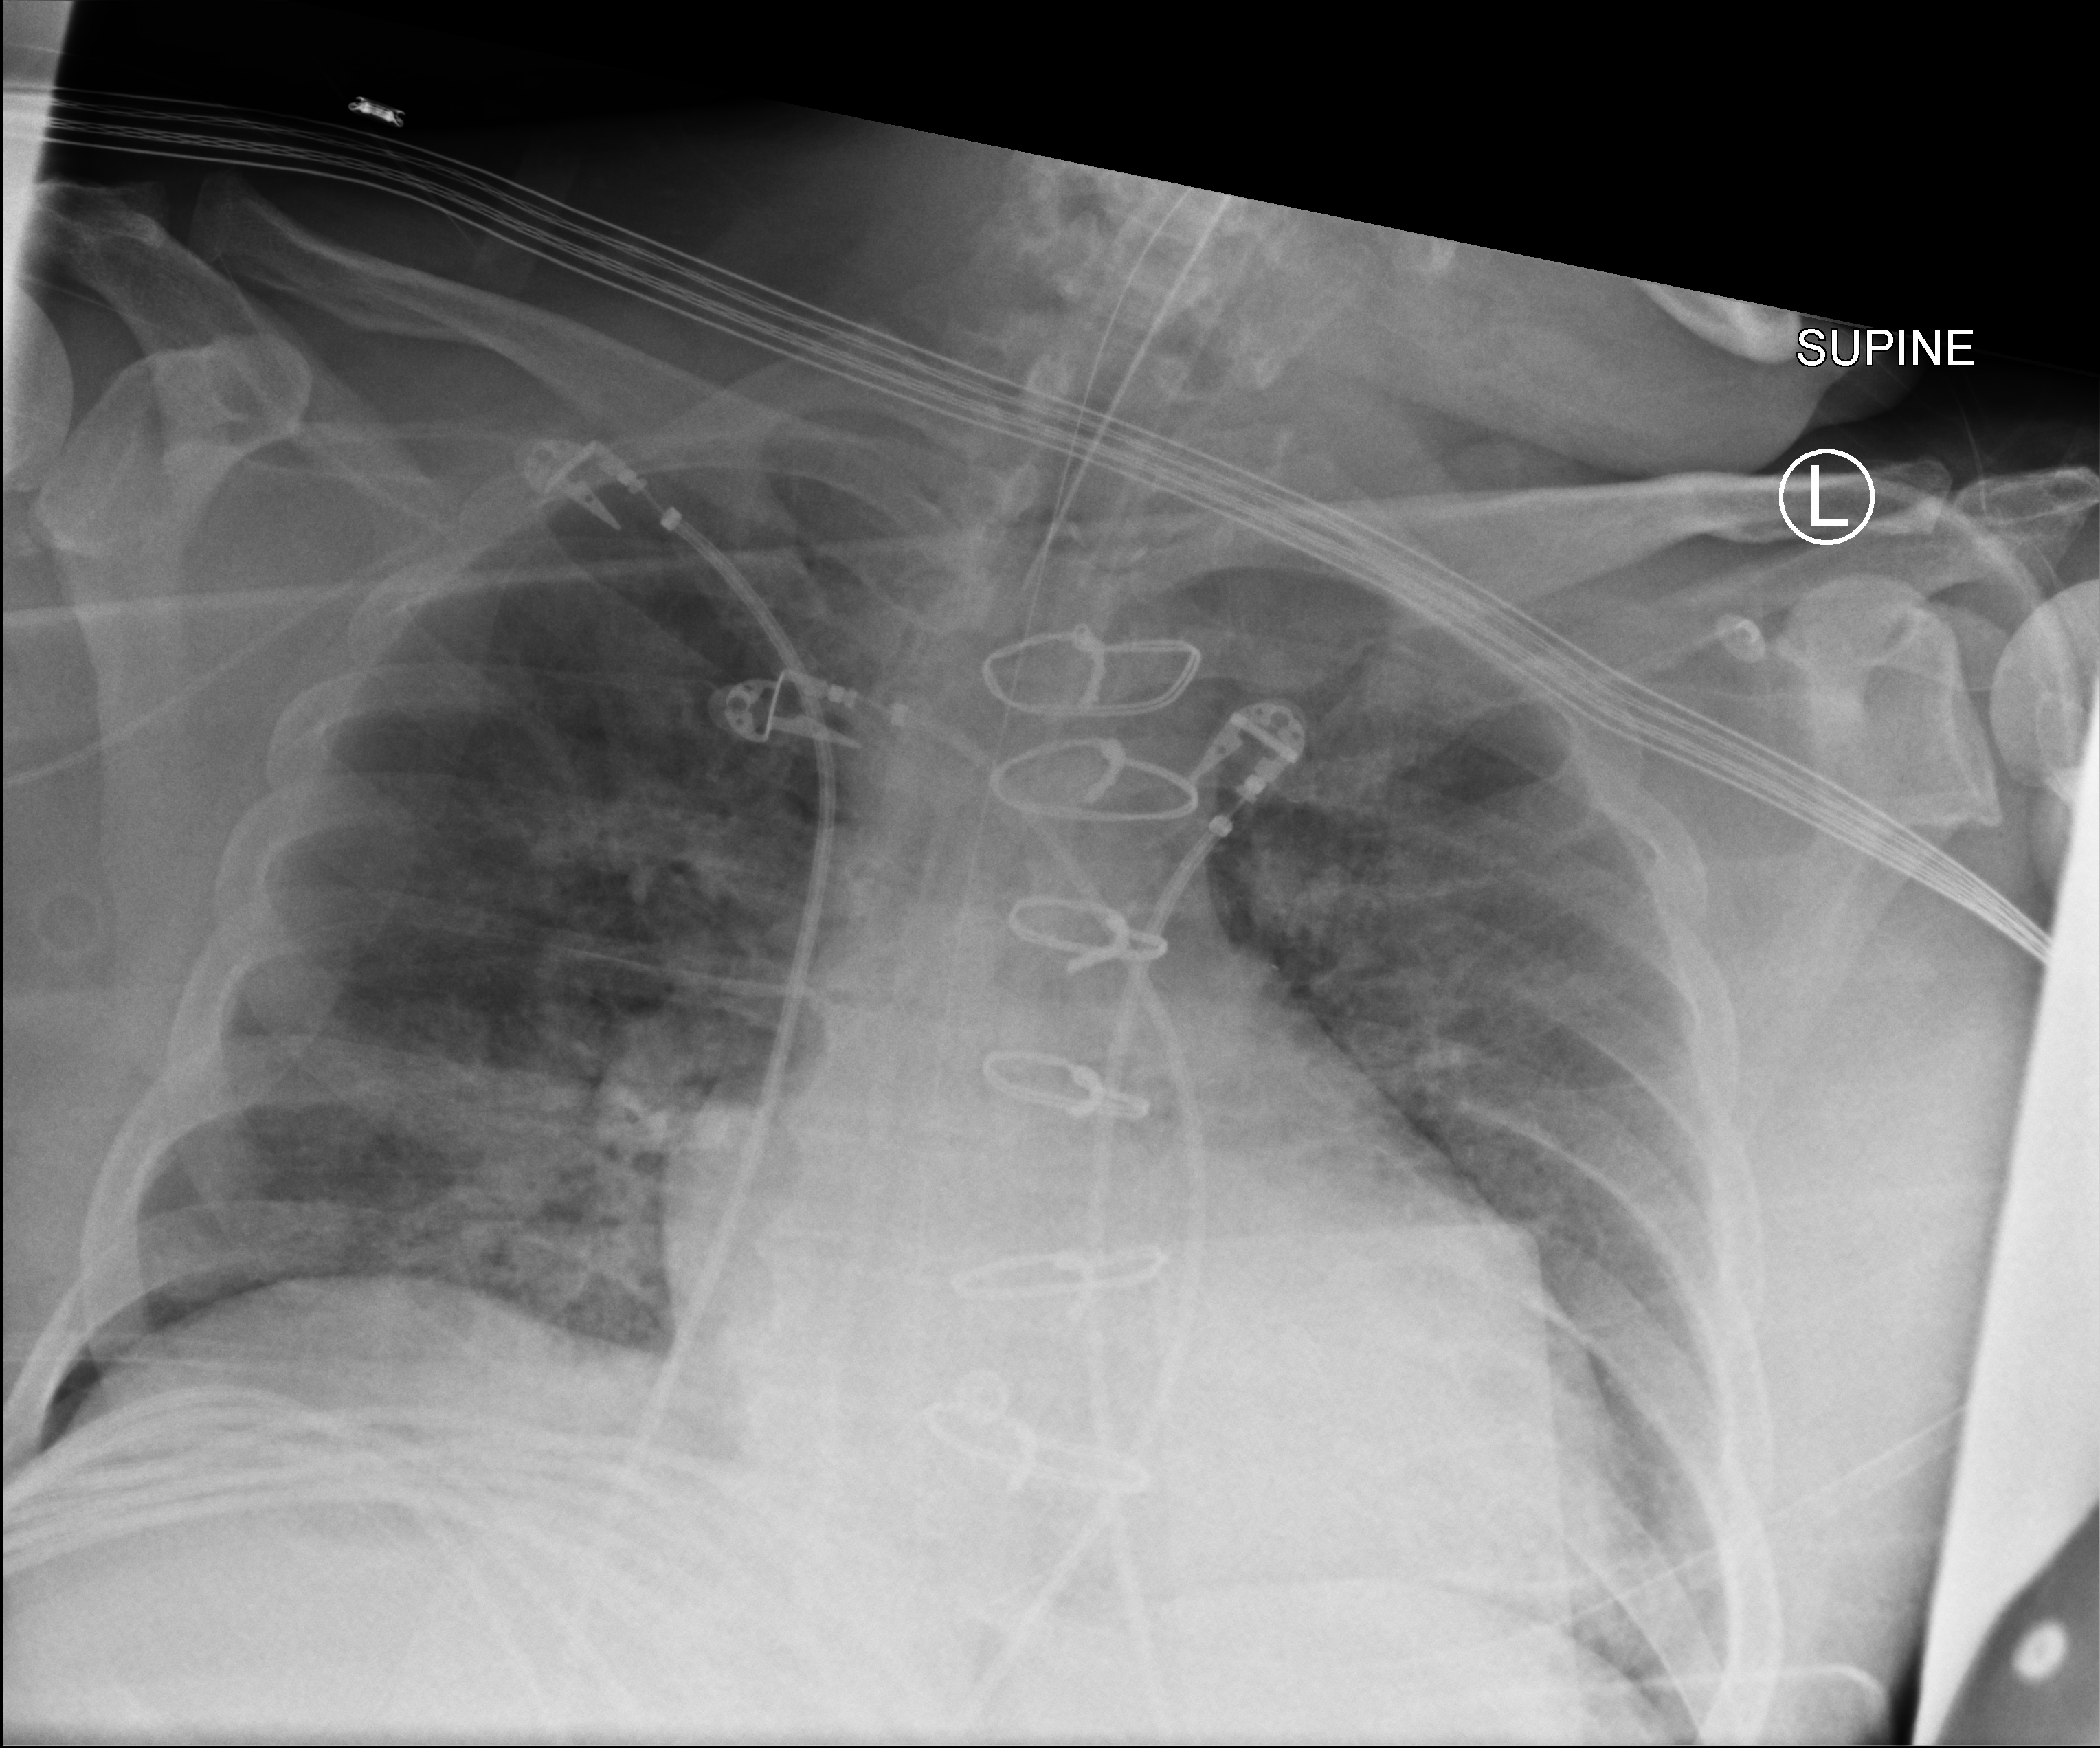
Bedside chest radiograph (computed radiography); anteroposterior (AP) projection. Adult patient hospitalised with COVID-19, age 18–59 years.
Admission-level facts for this patient (not findings on this image; timing relative to this image not recorded): admitted to intensive care during this hospital stay: yes; mechanically ventilated during this hospital stay: yes.